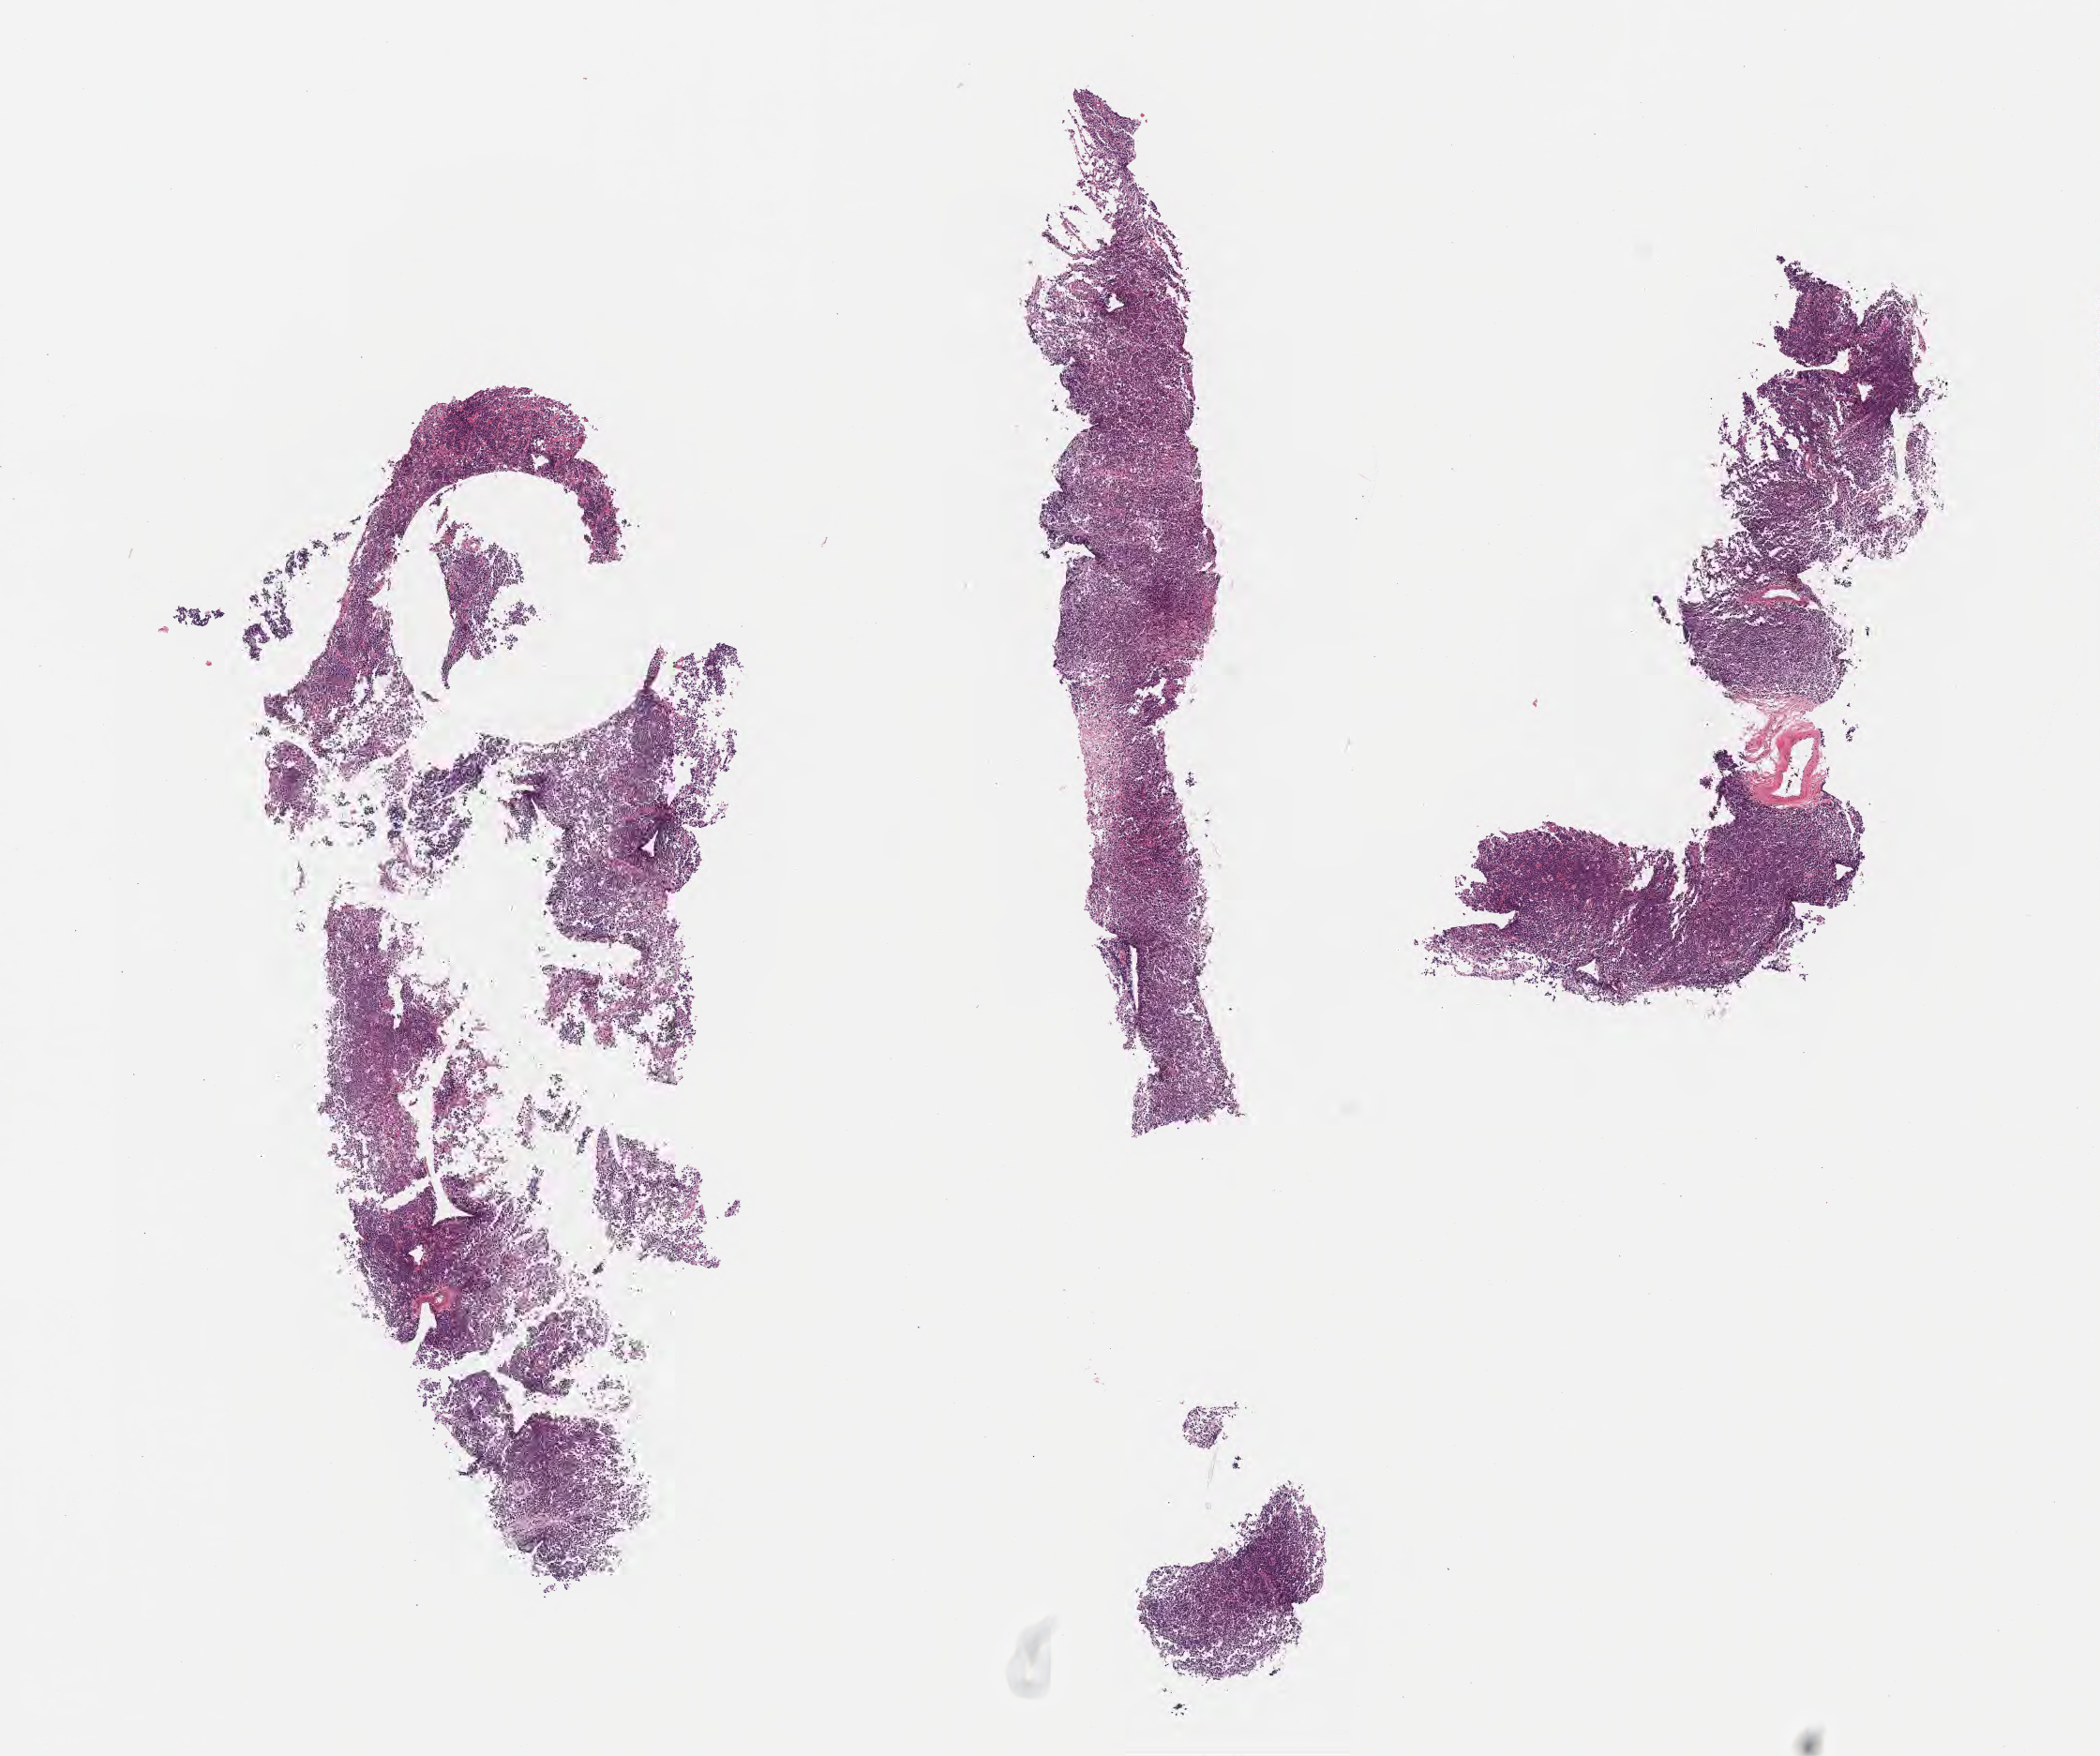
Whole-slide image, H&E stain, whole scanned area (about 9.1 x 7.6 mm) shown as a low-resolution overview. Tumor tissue. Anatomic site: spleen. Male, age 8 years at initial diagnosis.
Histologic diagnosis: Burkitt lymphoma, NOS.